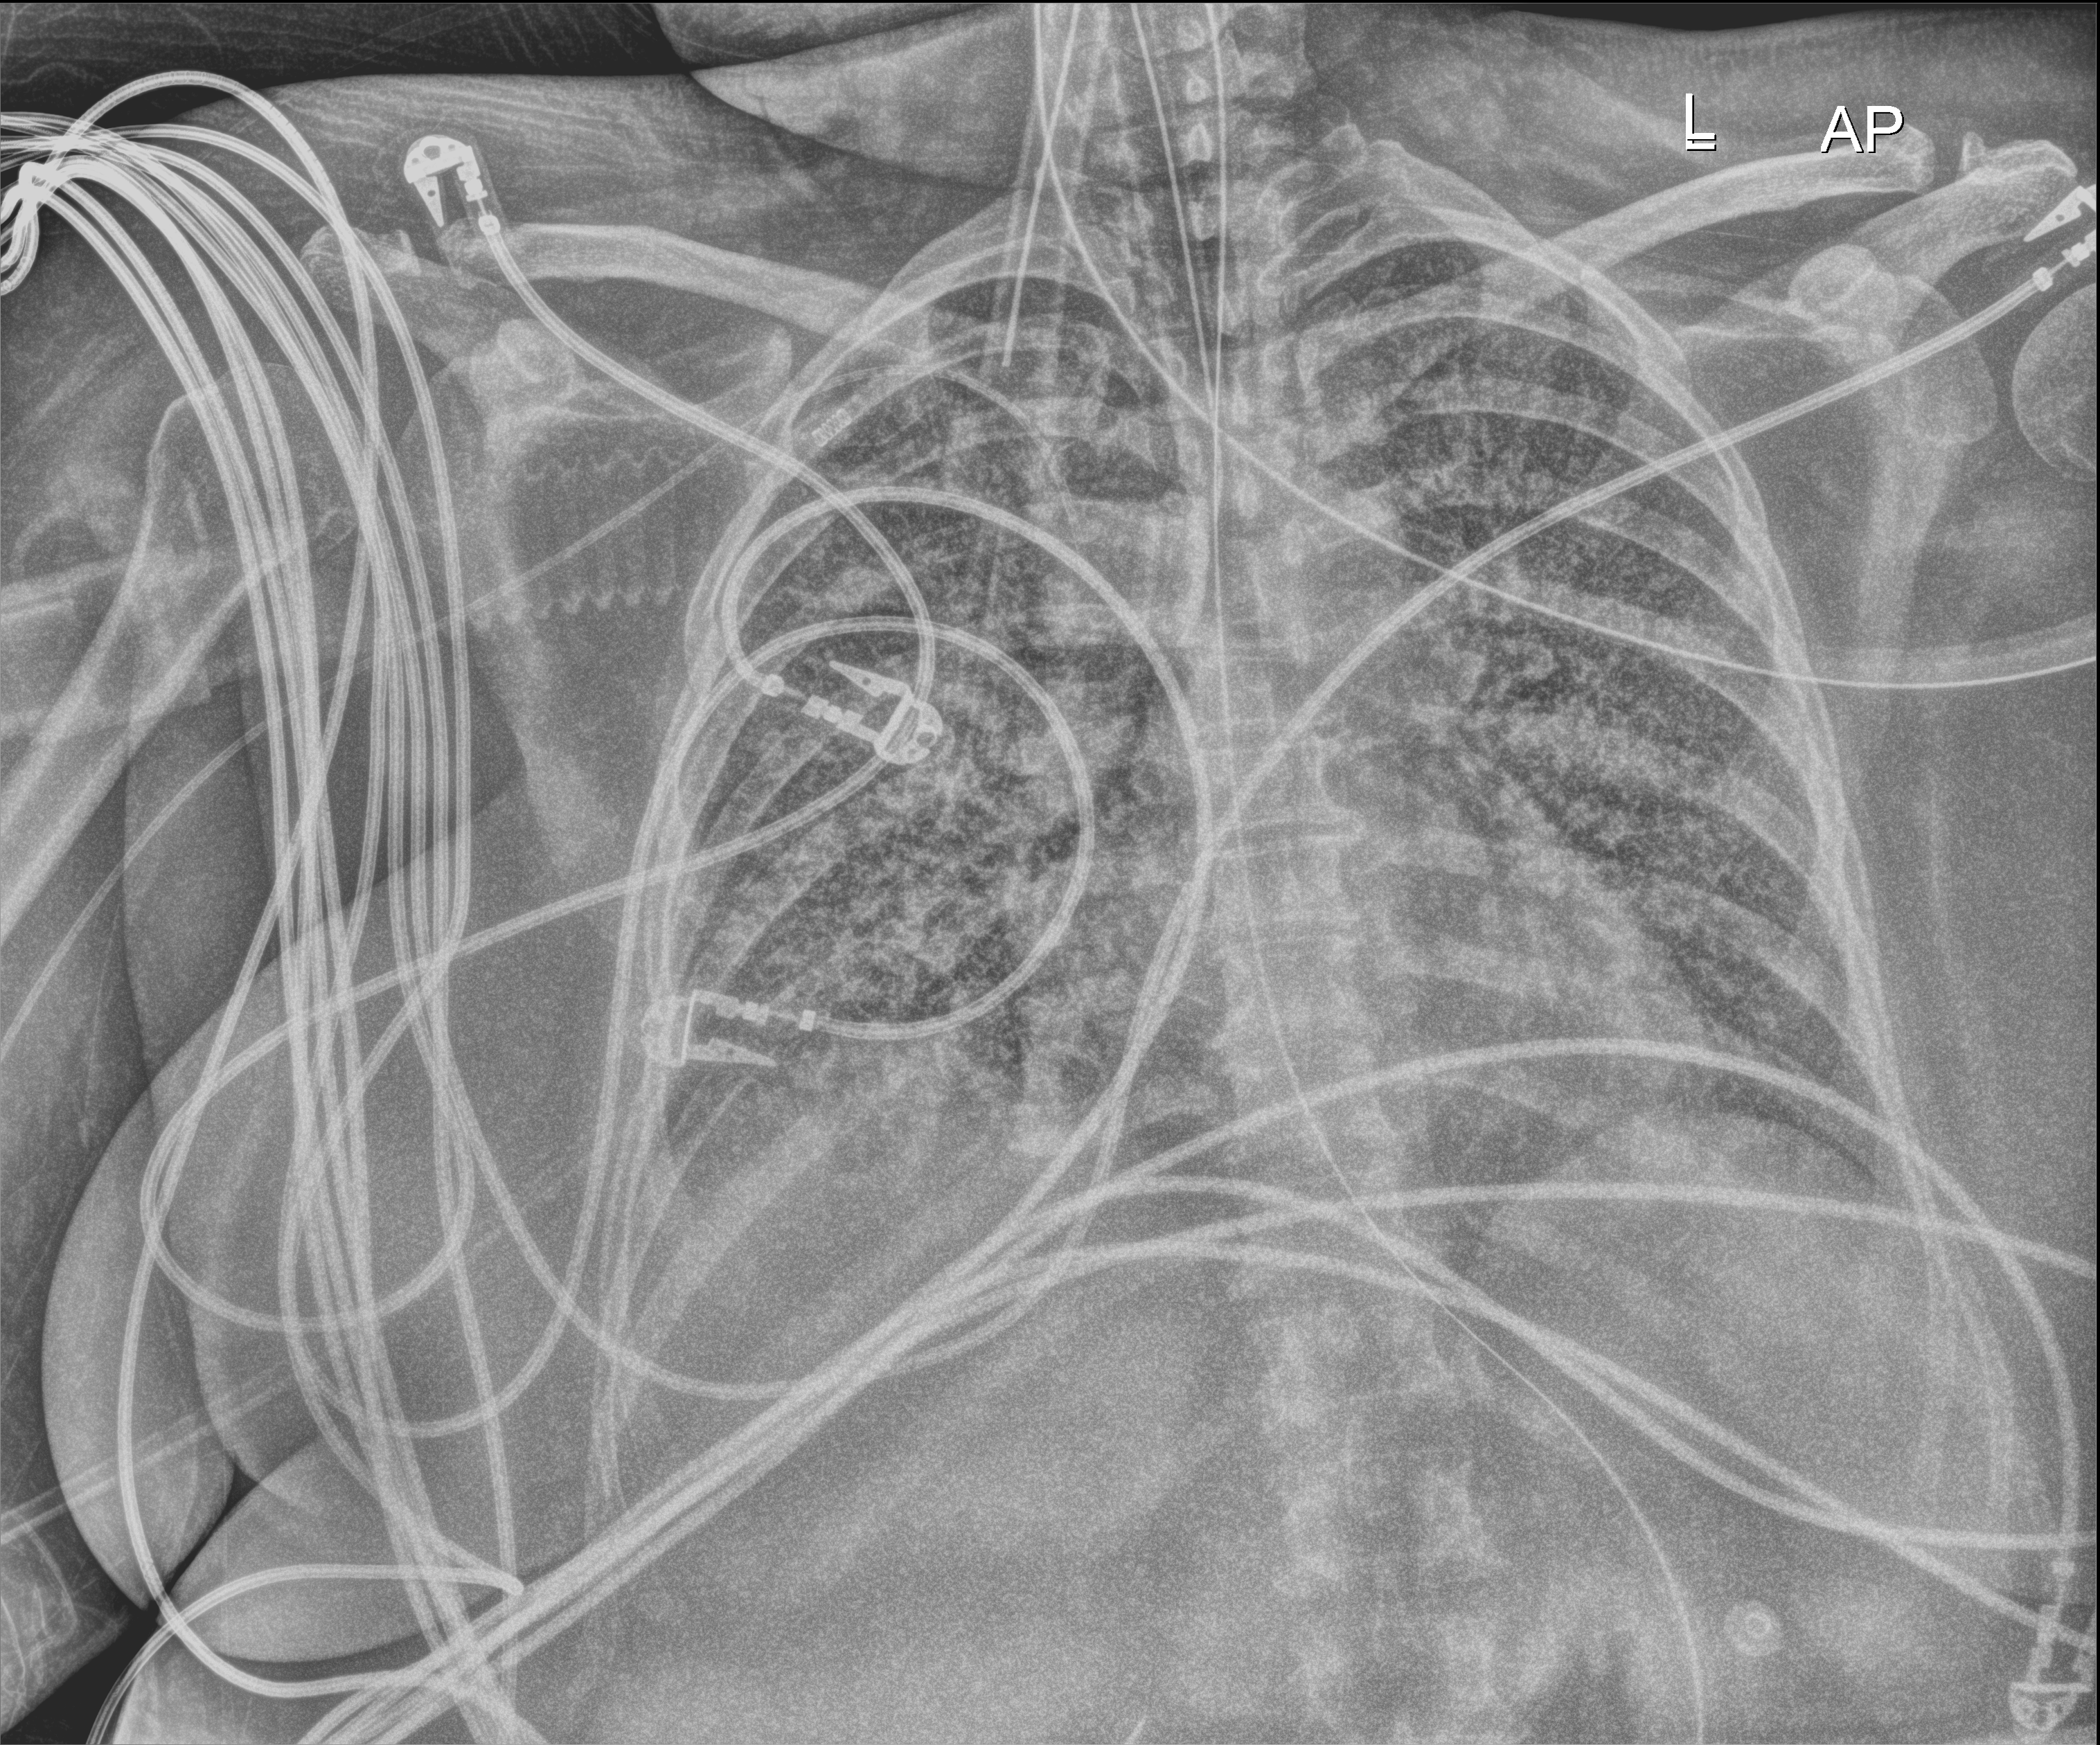
Chest X-ray (portable); anteroposterior (AP) projection. Female patient hospitalised with COVID-19, age 18–59 years.
From the hospital-stay record, not from the radiograph (when in the stay this image was taken is not recorded): mechanically ventilated during this hospital stay: yes; admitted to intensive care during this hospital stay: yes; diabetes (admission record): no.